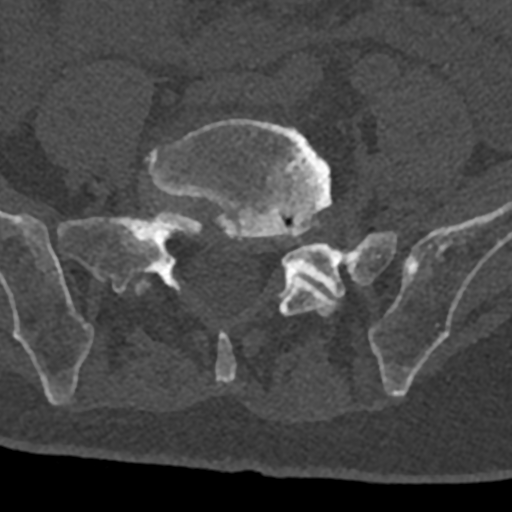
CT including the spine, one axial slice. Position 177 of 797 along the scan axis. 120 kVp. Bone window (W 1800 / L 400 HU). 0.5 mm slice thickness. 512 × 512 image matrix. Male patient, age 74 years. From the clinical record (not read from this slice): primary cancer: renal; vertebrae with lytic lesions (as recorded): T10, L1, L2, L3, L4, L5.
Annotated regions visible in this slice (semi-automatically segmented with operator editing):
- L5 vertebra: bounding box <135,118,352,384> (left, top, right, bottom; pixels)